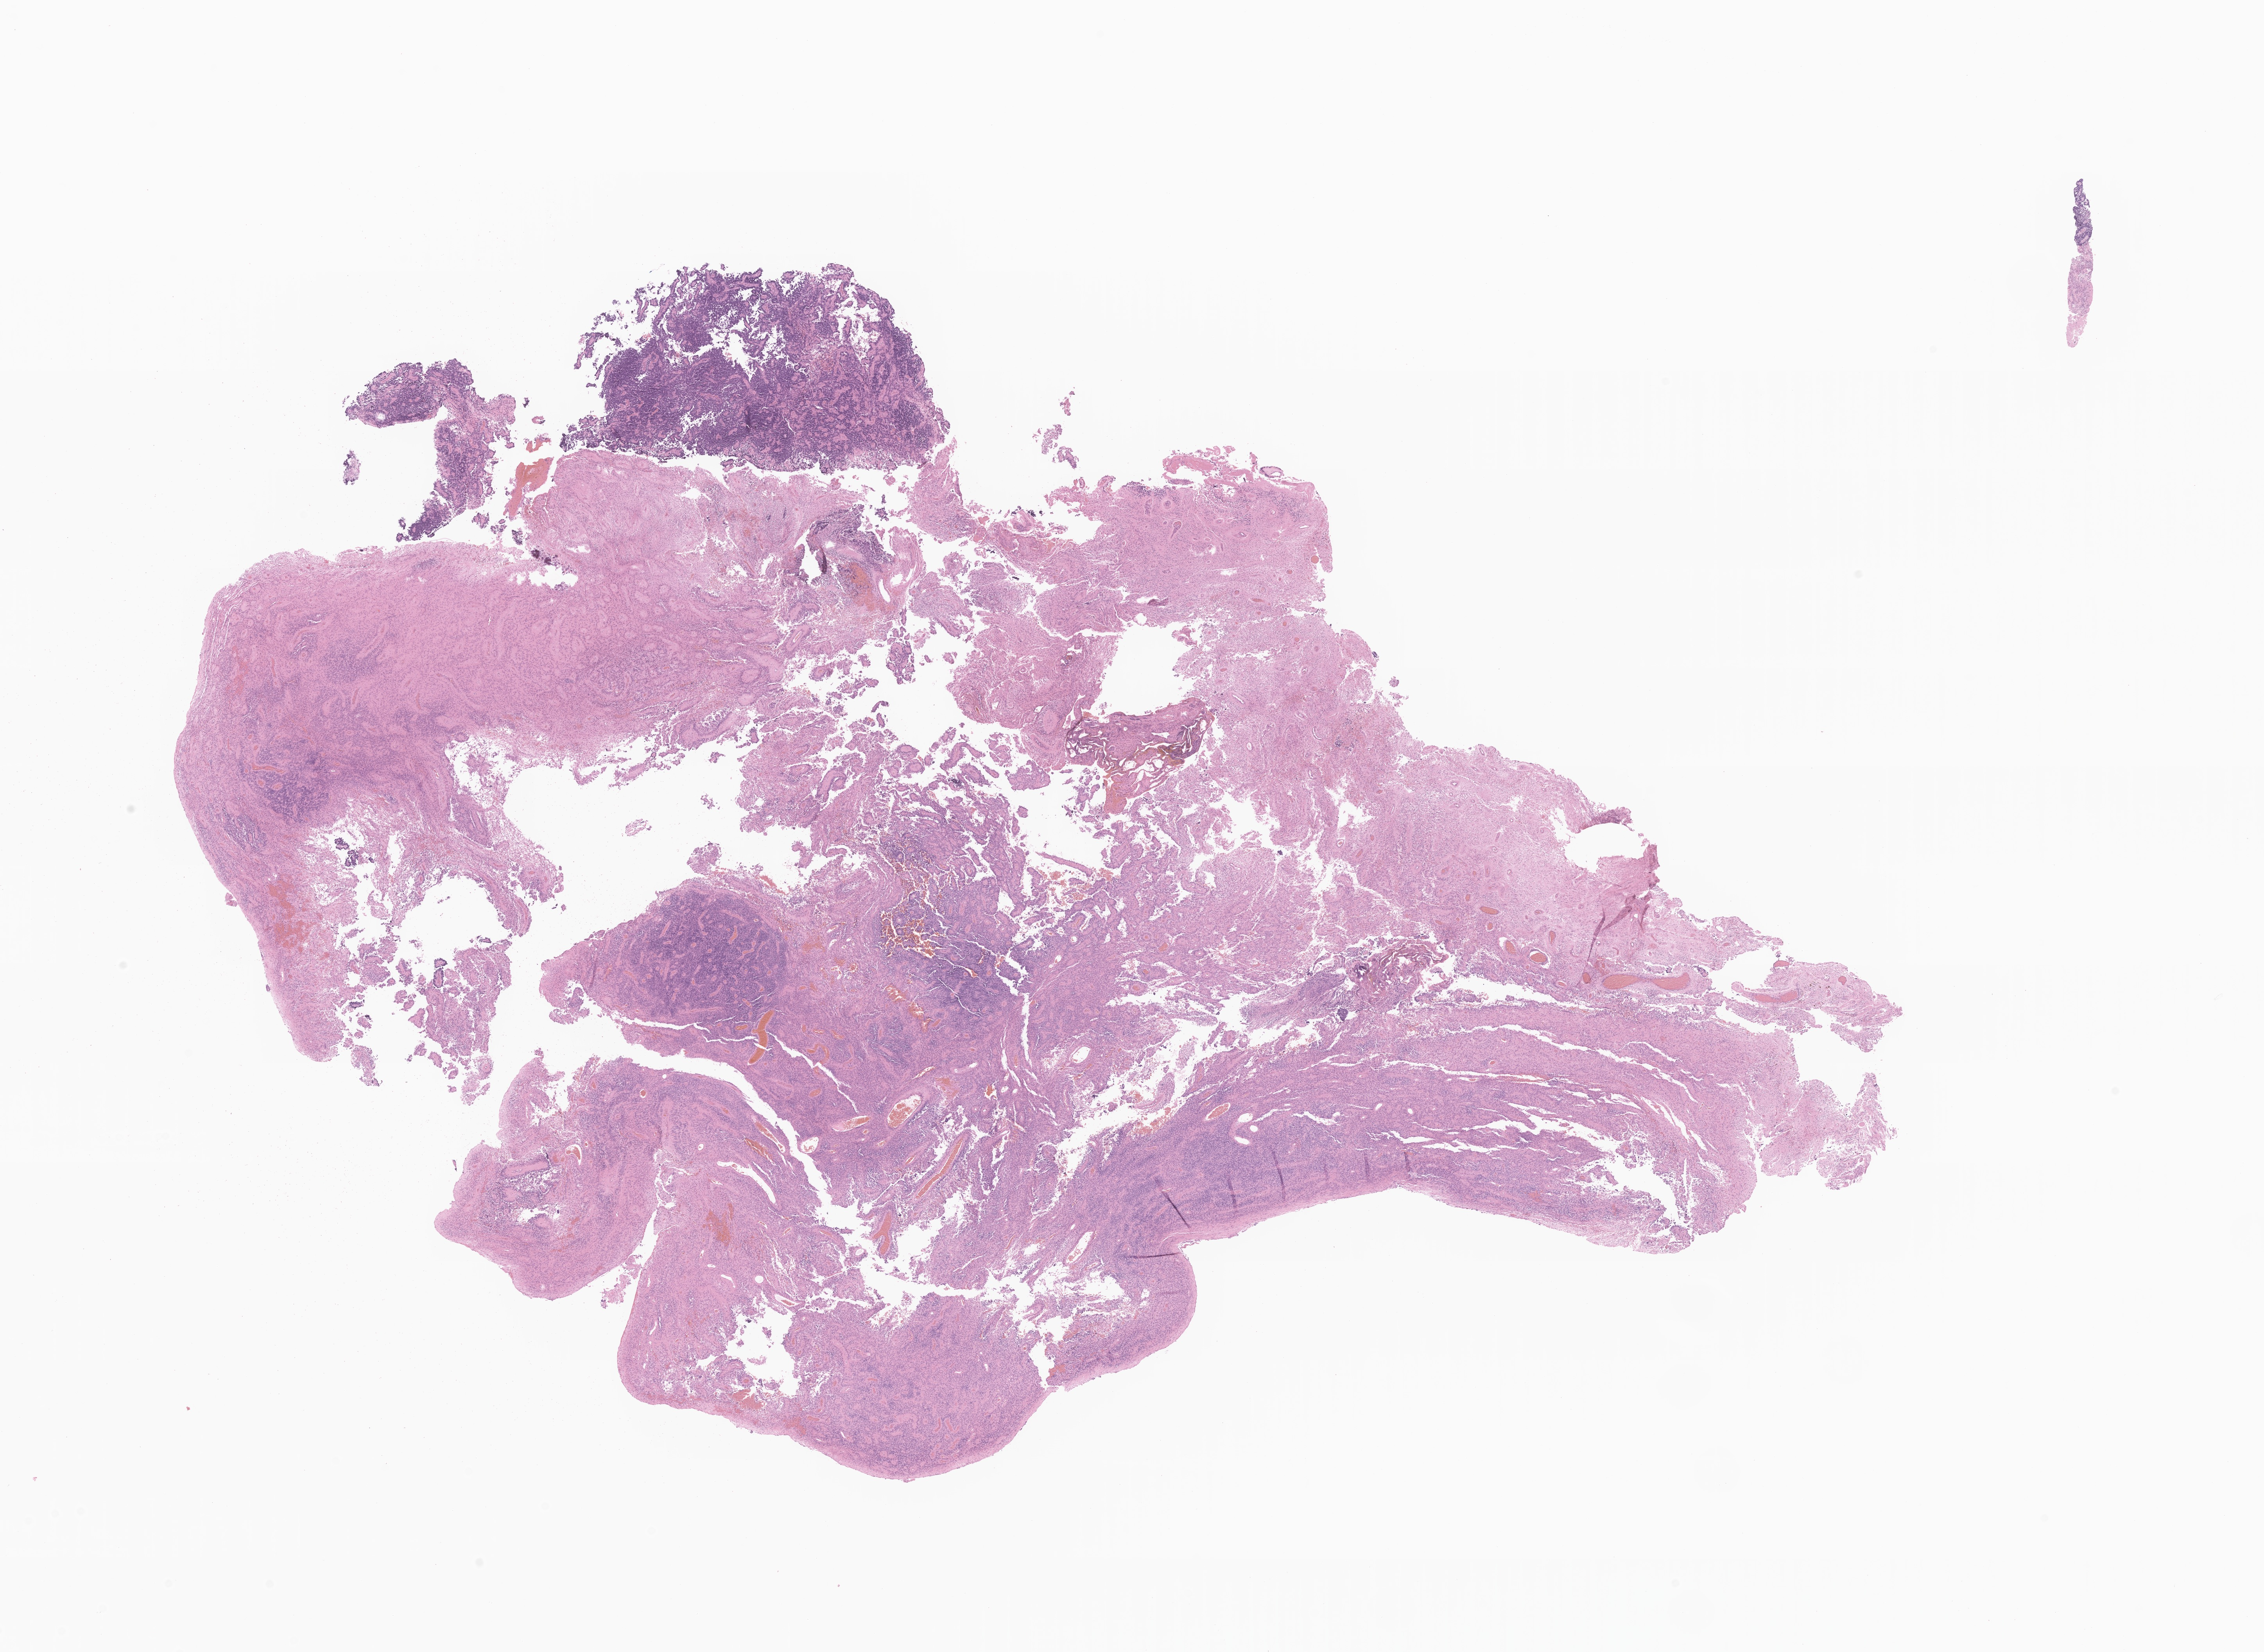
Whole-slide image, haematoxylin and eosin stain of tumor tissue from the cerebellum, whole scanned area (about 24.4 x 17.8 mm) shown as a low-resolution overview, FFPE section. Patient male; age 74 months (6 years 2 months).
Recorded diagnosis: Ependymoma, NOS.